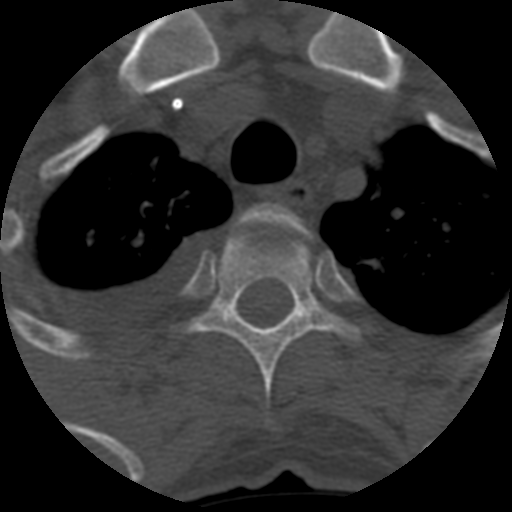
CT including the spine, one axial slice. Slice 490 of 708 in the series (ordered by position). 120 kVp. One of 3 acquisitions stored at this slice position. Bone window (W 1800 / L 400 HU). 1.25 mm slice thickness. 512 × 512 image matrix, field of view 160 × 160 mm. Patient age 55 years. From the clinical record (not read from this slice): primary cancer: colon; vertebrae with lytic lesions (as recorded): T12, L1, L5.
Structures marked on this image (semi-automatic segmentation, software-assisted and operator-edited):
- T2 vertebra: bounding box (x1, y1, x2, y2) in pixels: (237, 204, 300, 228)
- T3 vertebra: (192, 222, 354, 423)